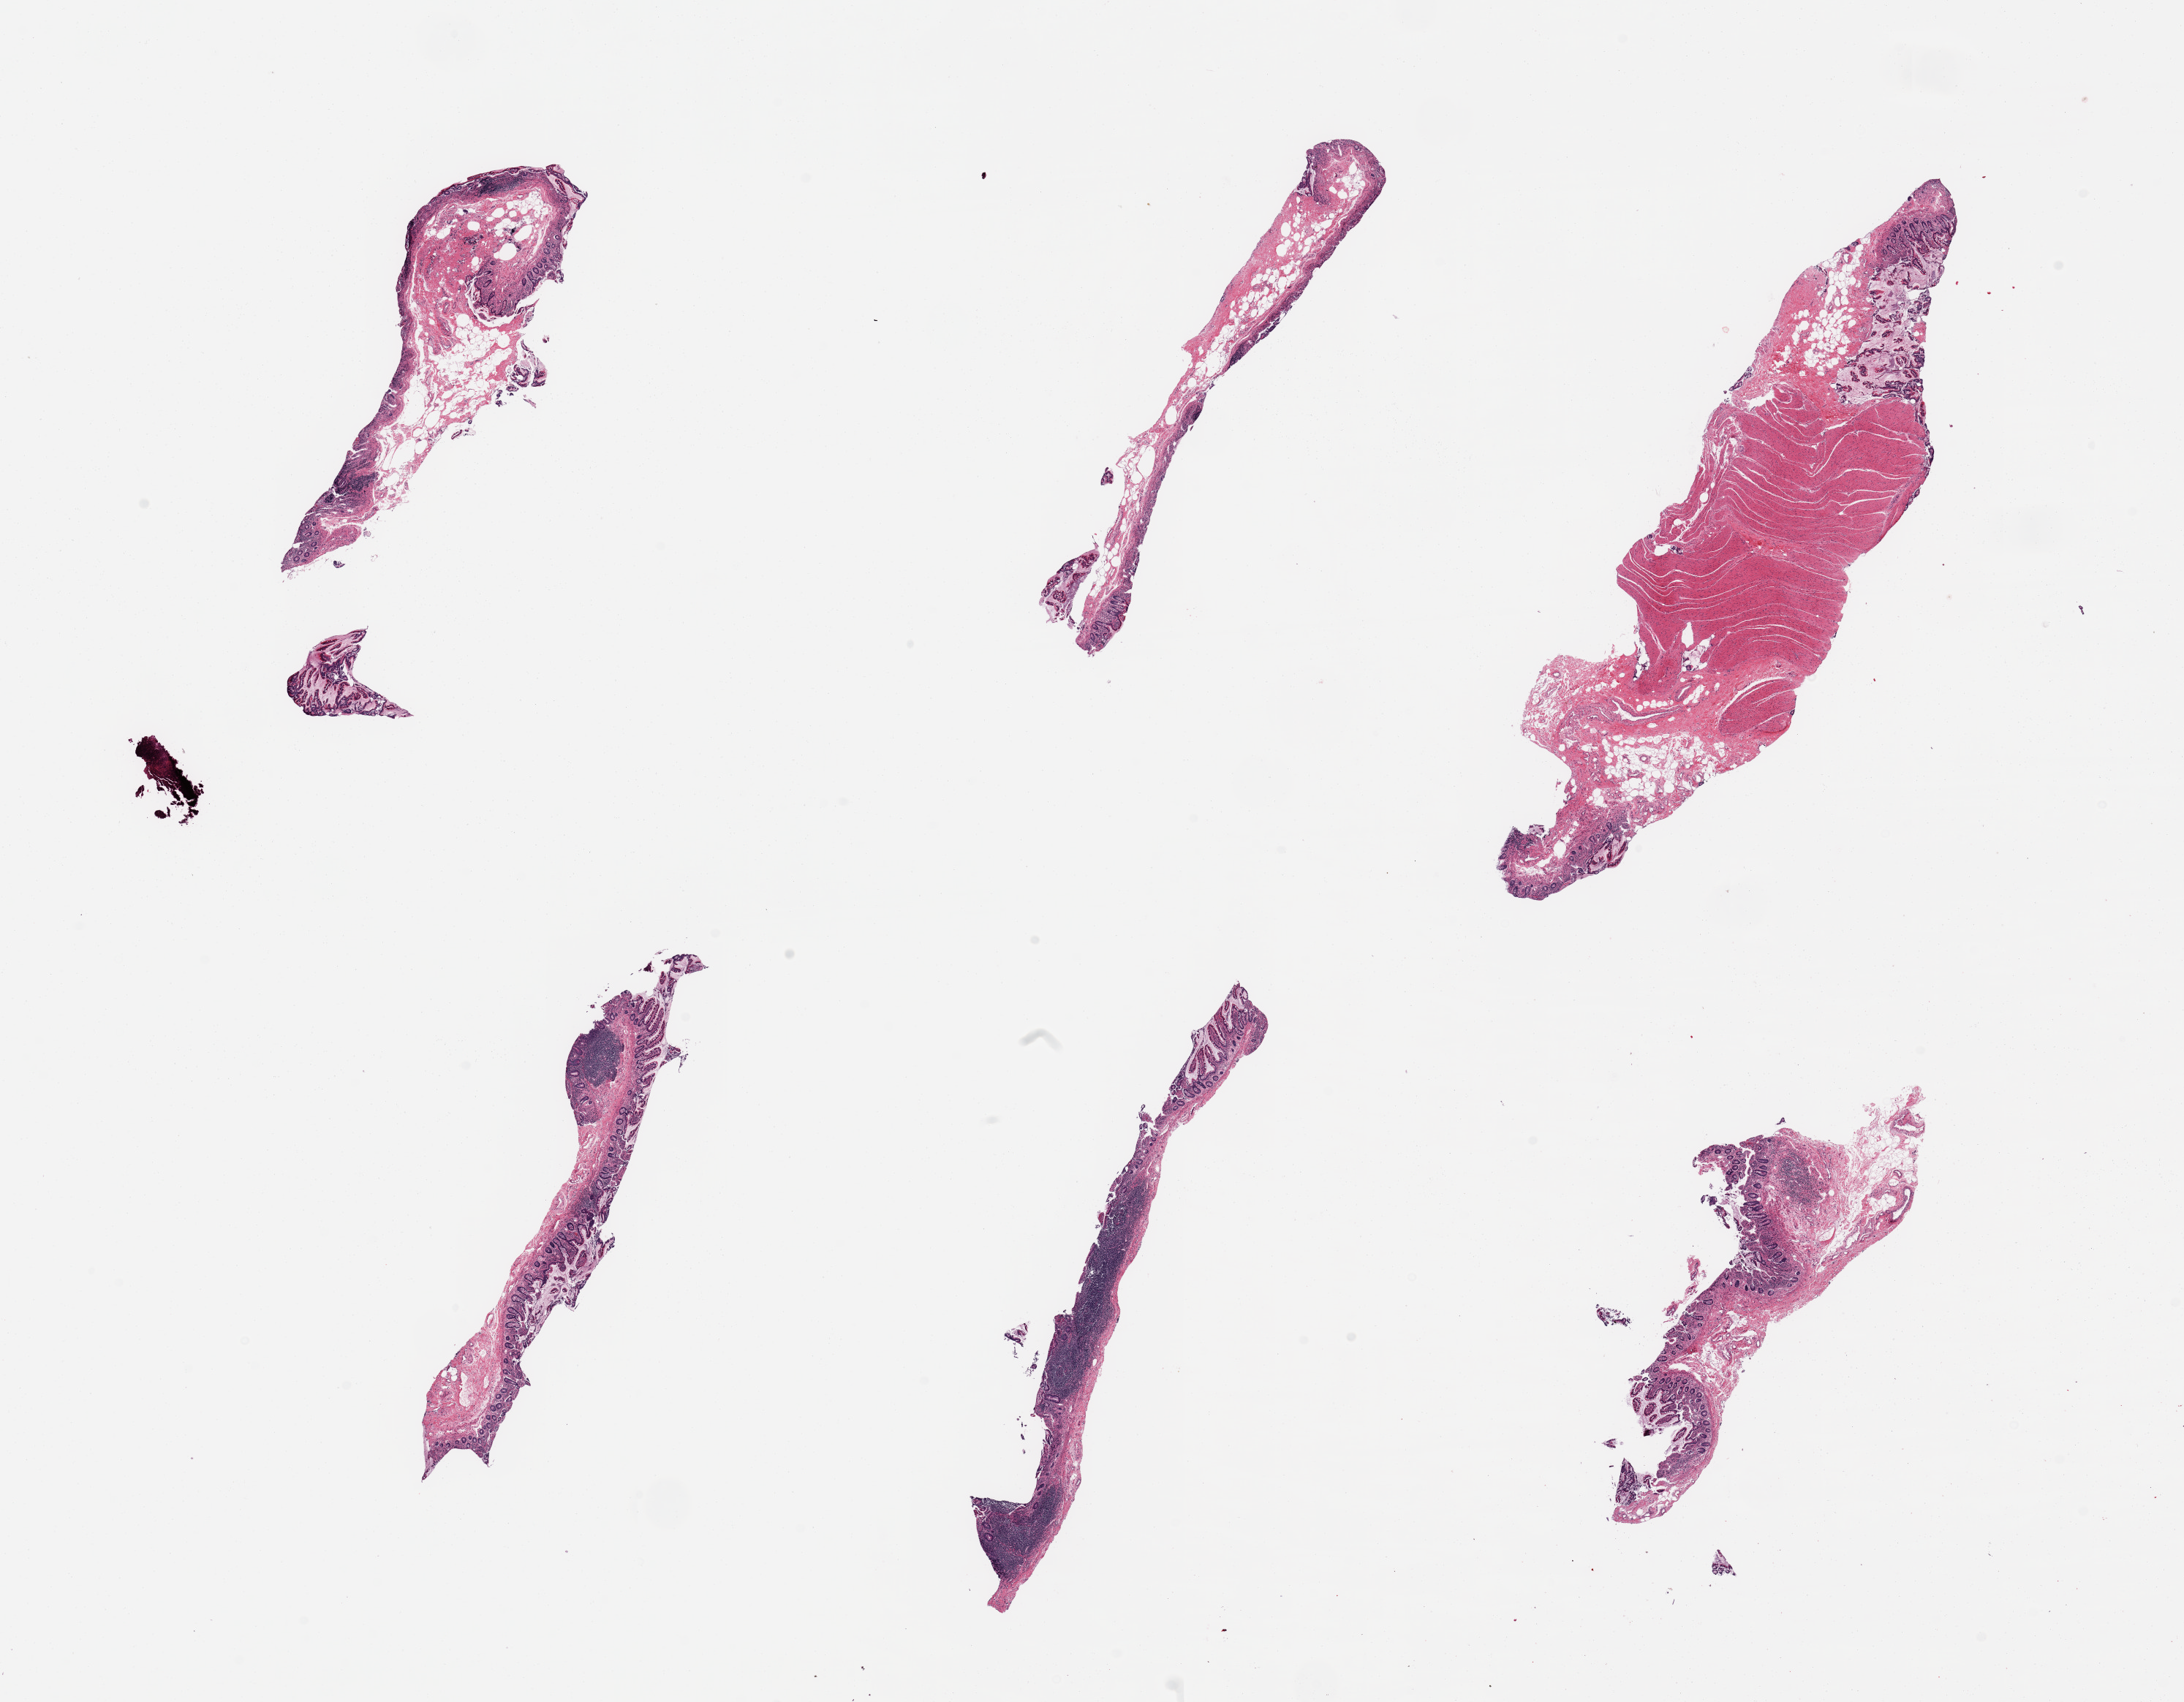
Haematoxylin and eosin whole-slide image, brightfield, a low-resolution overview of the entire scanned area, about 23.6 x 18.4 mm (from a 20x scan); PAXgene-fixed, paraffin-embedded tissue; target tissue: ileum; tissue donor sample. Donor sex: male.
• pathologist's review note for this sample: 6 pieces, ~20% target lymphoid aggregates